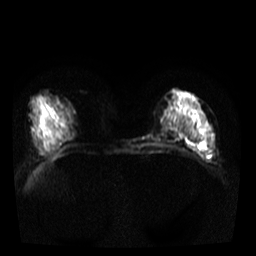
Breast MRI, one axial slice. Position 17 of 40 along the scan axis. Diffusion-weighted series; image 2 of 4 stored at this slice position (different b-values; order by instance number). 3 T. 5 mm slice thickness. 256 × 256 image matrix. Female patient.
Outlined on this slice (expert manual segmentation):
- tumour on diffusion-weighted imaging: bounding box (x1, y1, x2, y2) in pixels: (206, 151, 211, 158)